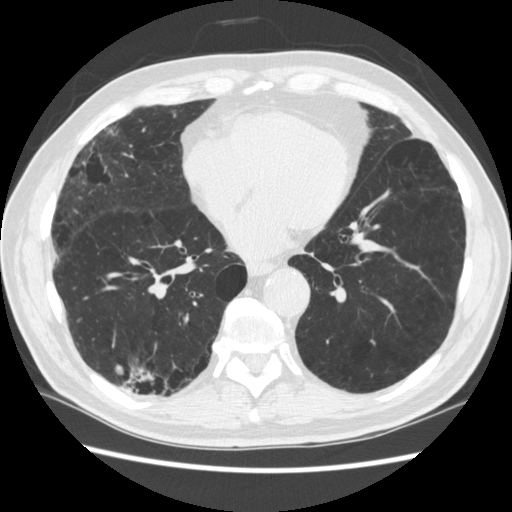
Axial slice from a low-dose chest CT screening exam, third screening round (two years after baseline), lung window (W 1500 / L -600 HU), 1.25 mm slice thickness, slice 160 of 266 in the series, 512 × 512 image matrix, field of view 360 × 360 mm. Male, age 70 years at enrolment. Former smoker at enrolment.
Expert-annotated lung lesion, bounding box (x1, y1, x2, y2) in pixels: (129, 359, 178, 414). The screening reader recorded 4 non-calcified nodules or masses ≥4 mm on this exam (right lower lobe, right lower lobe, left lower lobe, left lower lobe); which of them this box marks is not recorded. Lung cancer was diagnosed 253 days after this screen: squamous cell carcinoma, NOS, right upper lobe, poorly differentiated (G3), stage IV (AJCC 6th edition).